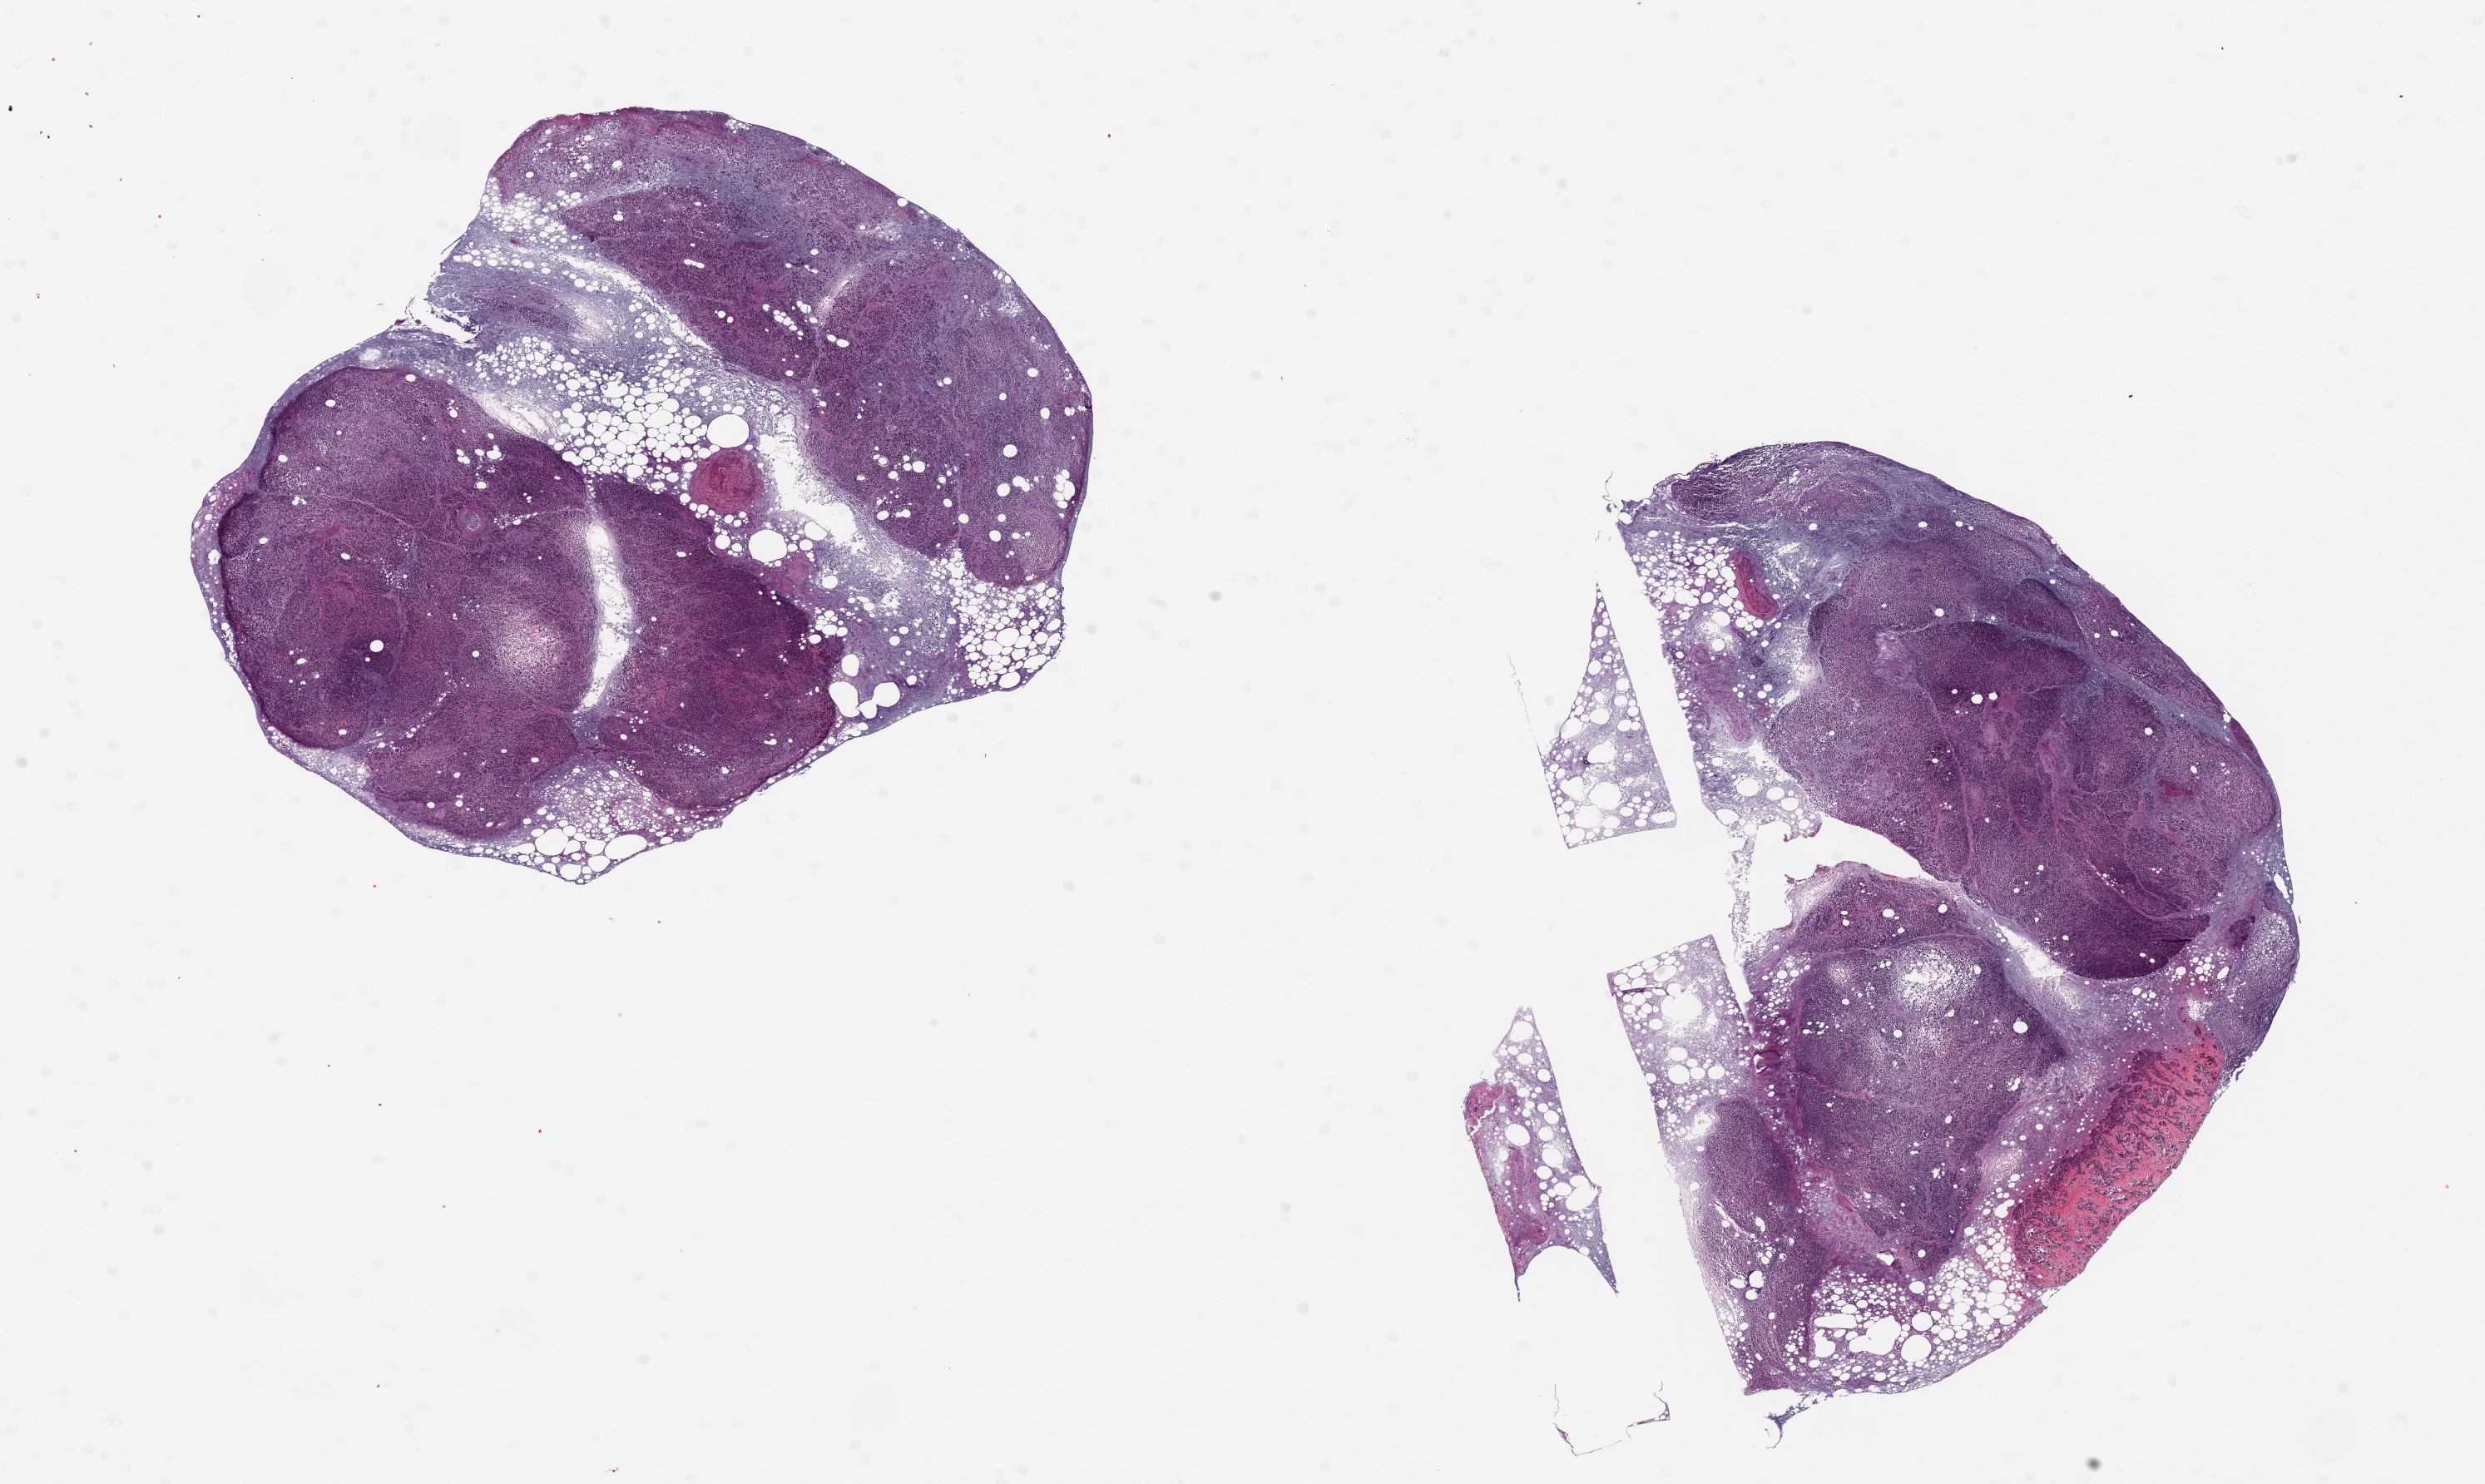
Whole-slide image, H&E stain — low-resolution overview of the scanned area, about 23.6 x 14.1 mm. PAXgene-fixed, paraffin-embedded tissue. Target tissue: pancreas. Tissue donor sample. Donor: male.
* reviewer comment on this tissue sample: 2 pieces, 8x7 & 9x8mm; tissue is unrecognizable due to high degree of autolysis and saponification of adipose